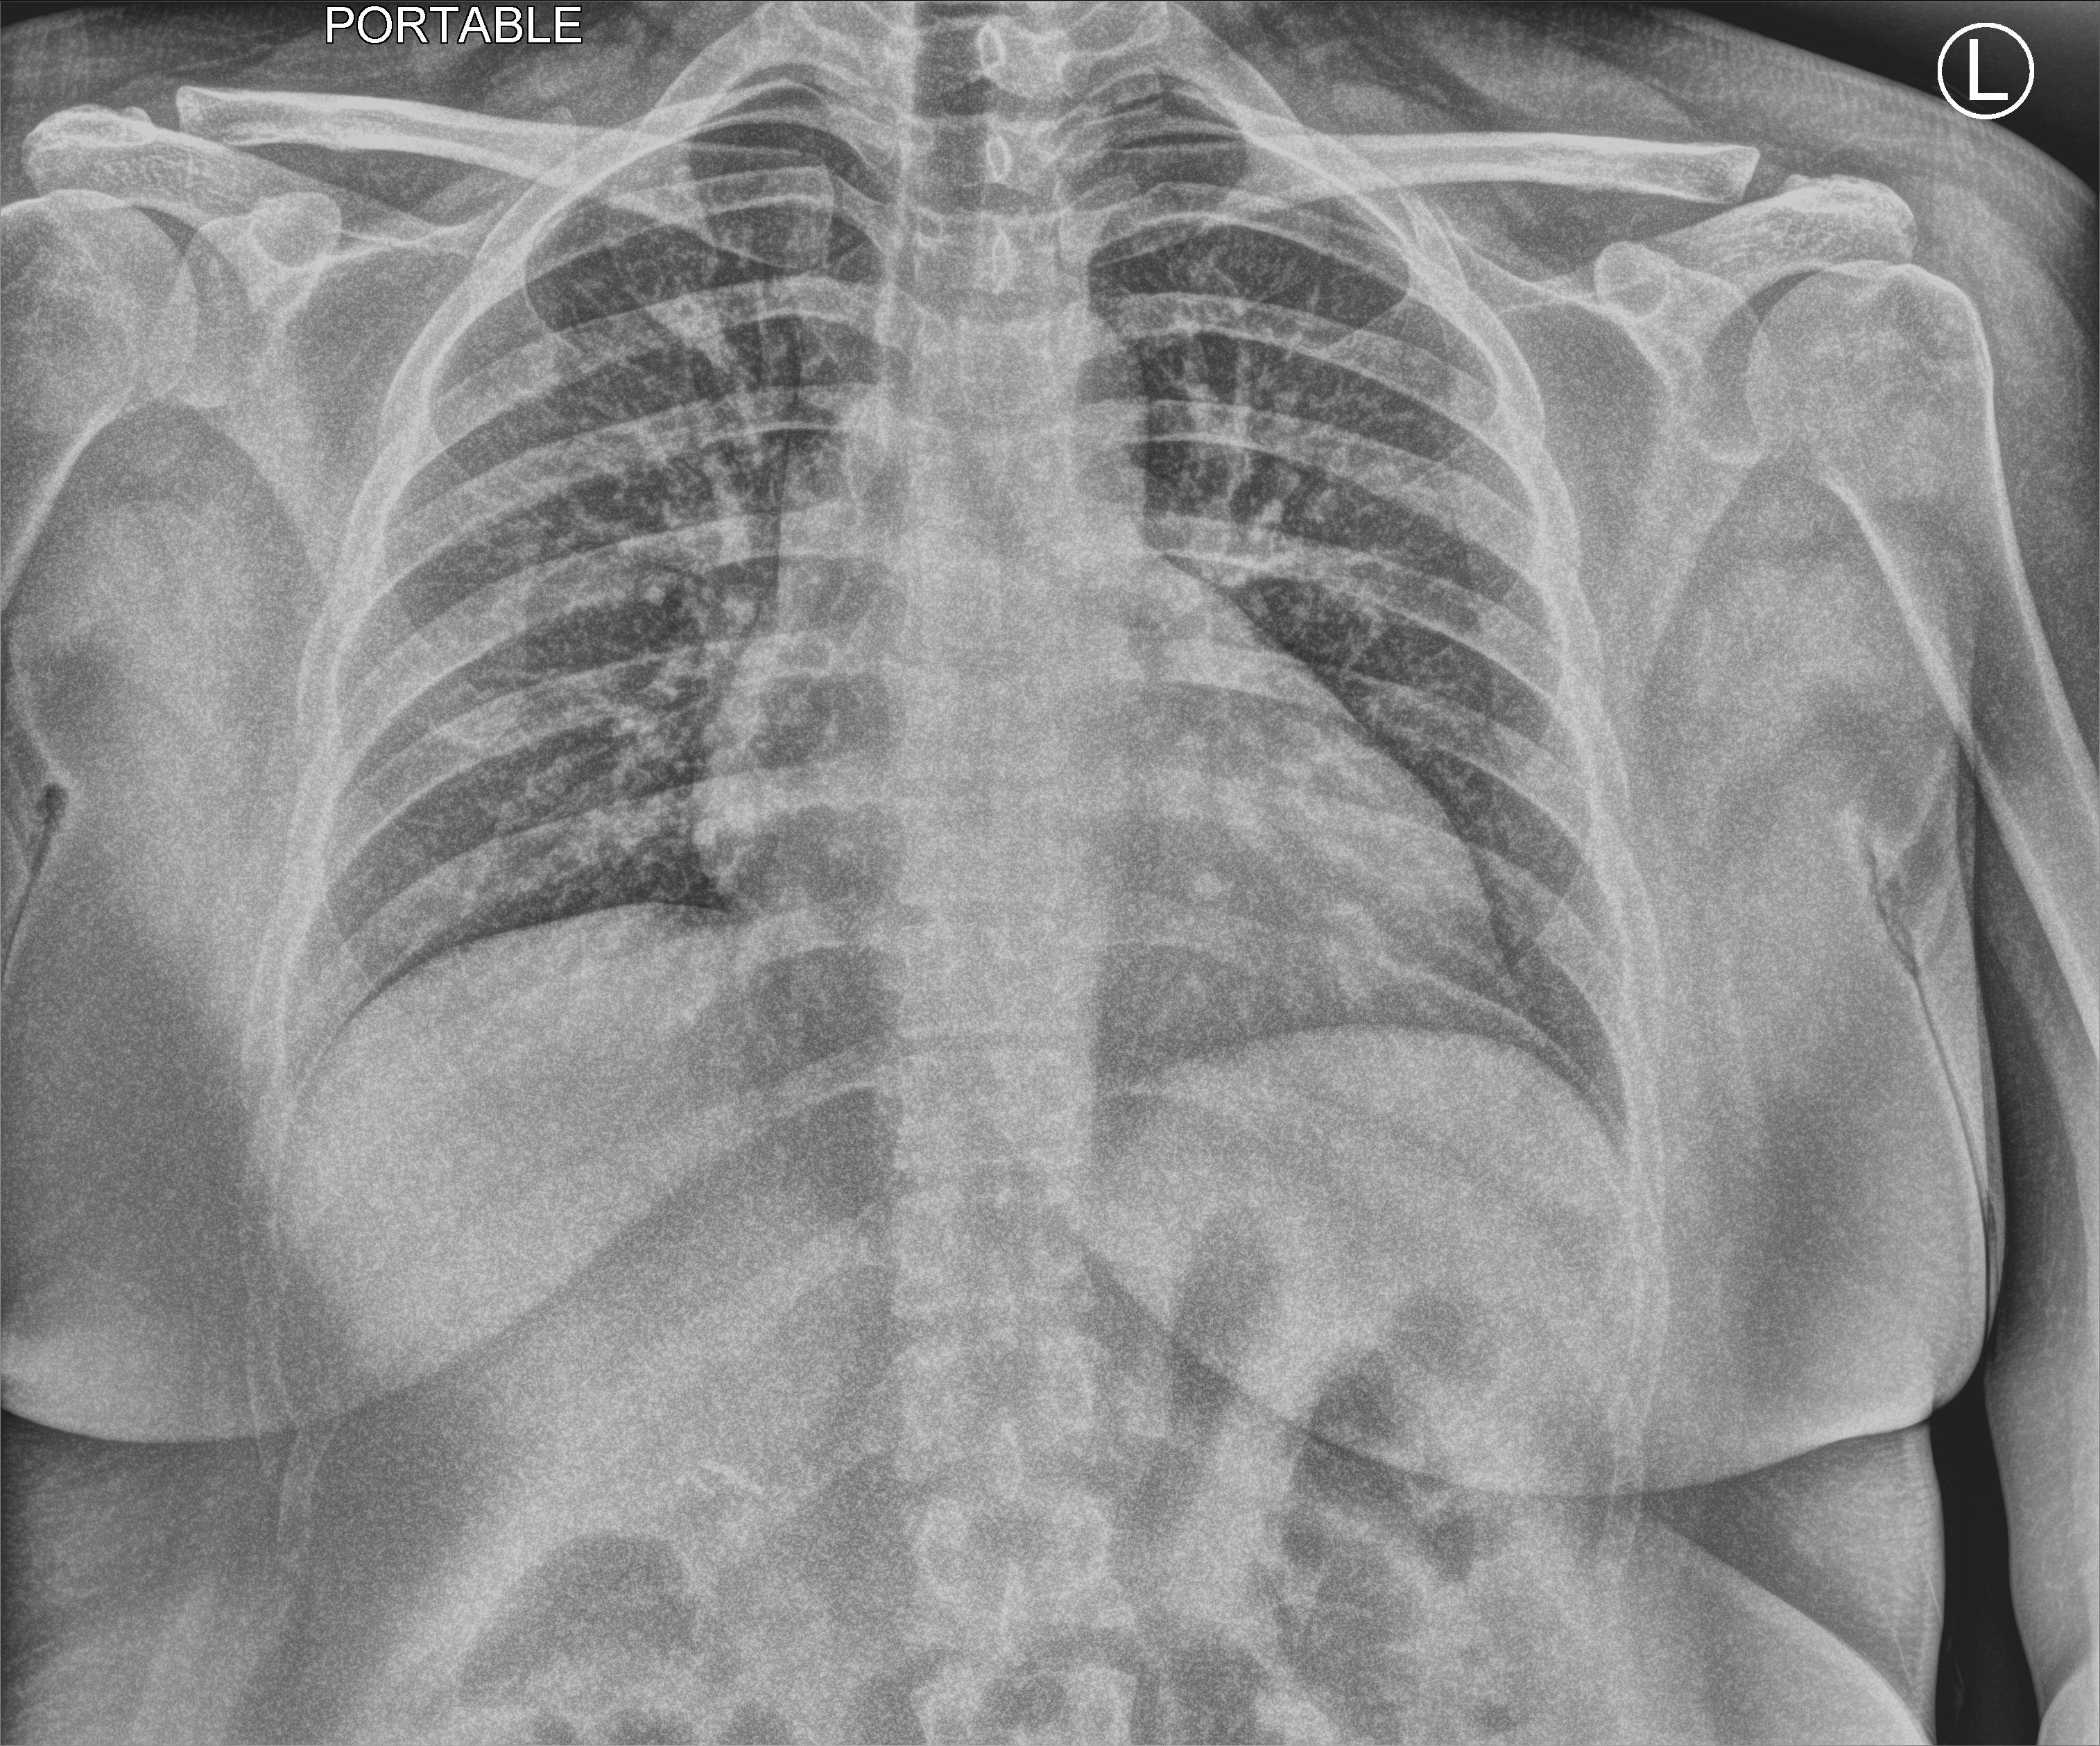
Chest X-ray (portable), anteroposterior (AP) projection. Female patient hospitalised with COVID-19, age 18–59 years.
From the hospital-stay record, not from the radiograph (when in the stay this image was taken is not recorded): smoking status (admission record): never; hypertension (admission record): no.